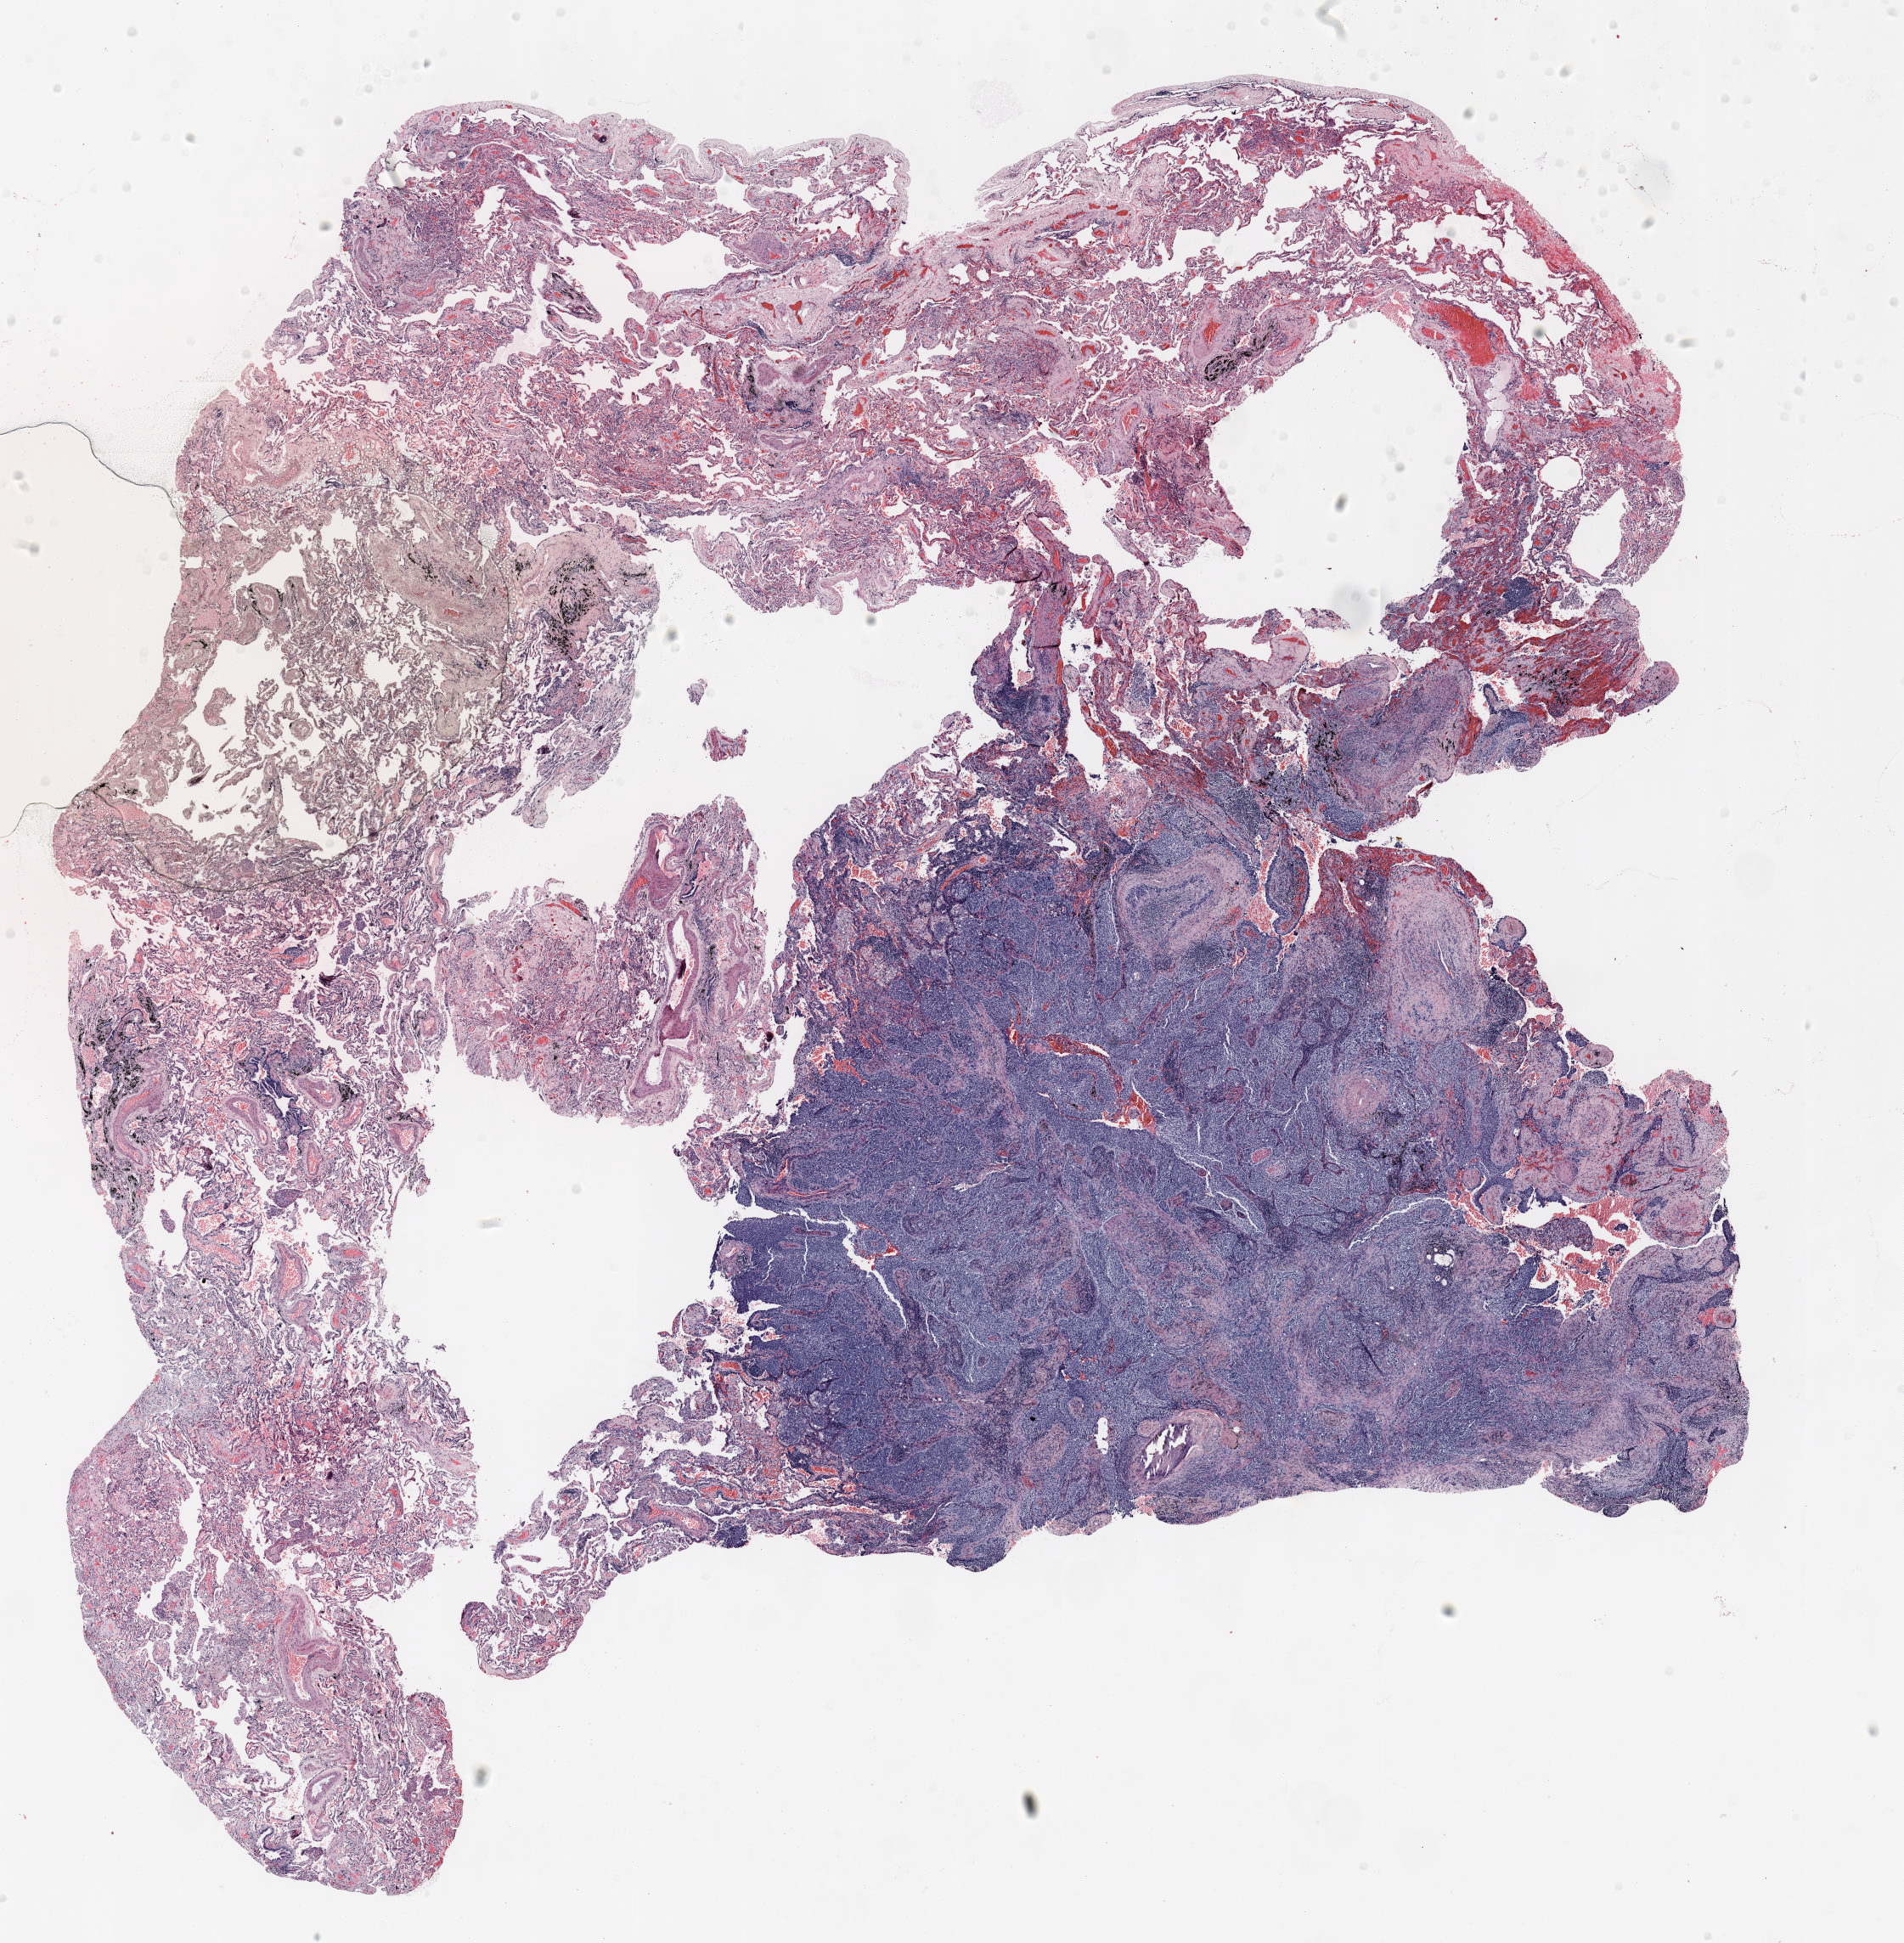
Whole-slide histology image, H&E-stained, low-resolution overview of the scanned area, about 18.0 x 18.4 mm (acquisition: 20x scan), FFPE section, lung tissue. Male patient, aged 58 at enrolment. Former smoker at enrolment. Grade: moderately differentiated (G2).
- tumour size (pathology): 18 mm
- stage (AJCC 6th edition): IB
- primary tumour location (clinical record): right upper lobe
- participant's lung-cancer diagnosis: Squamous cell carcinoma, NOS